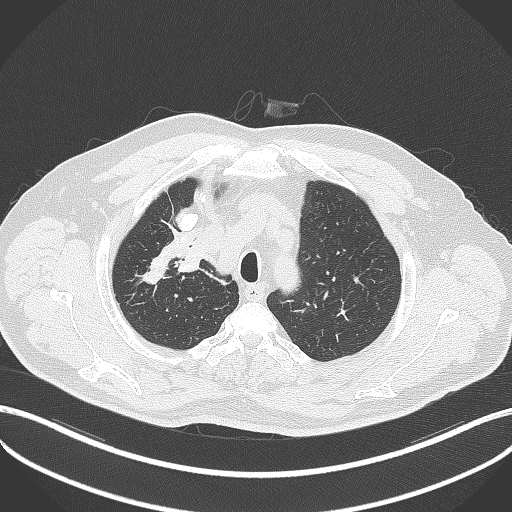
Chest CT, one axial slice. Position 317 of 411 along the scan axis. 120 kVp. Lung window (W 1500 / L -600 HU). 1 mm slice thickness. 512 × 512 image matrix, field of view 400 × 400 mm. Male patient, age 60 years. Case-level facts recorded for this patient, not image findings: clinical TNM (as recorded): T1b N1 M0.
Outlined on this slice (bounding box drawn by a radiologist):
- lung tumour (recorded histology: squamous cell carcinoma): bounding box <174,233,202,274> (left, top, right, bottom; pixels)